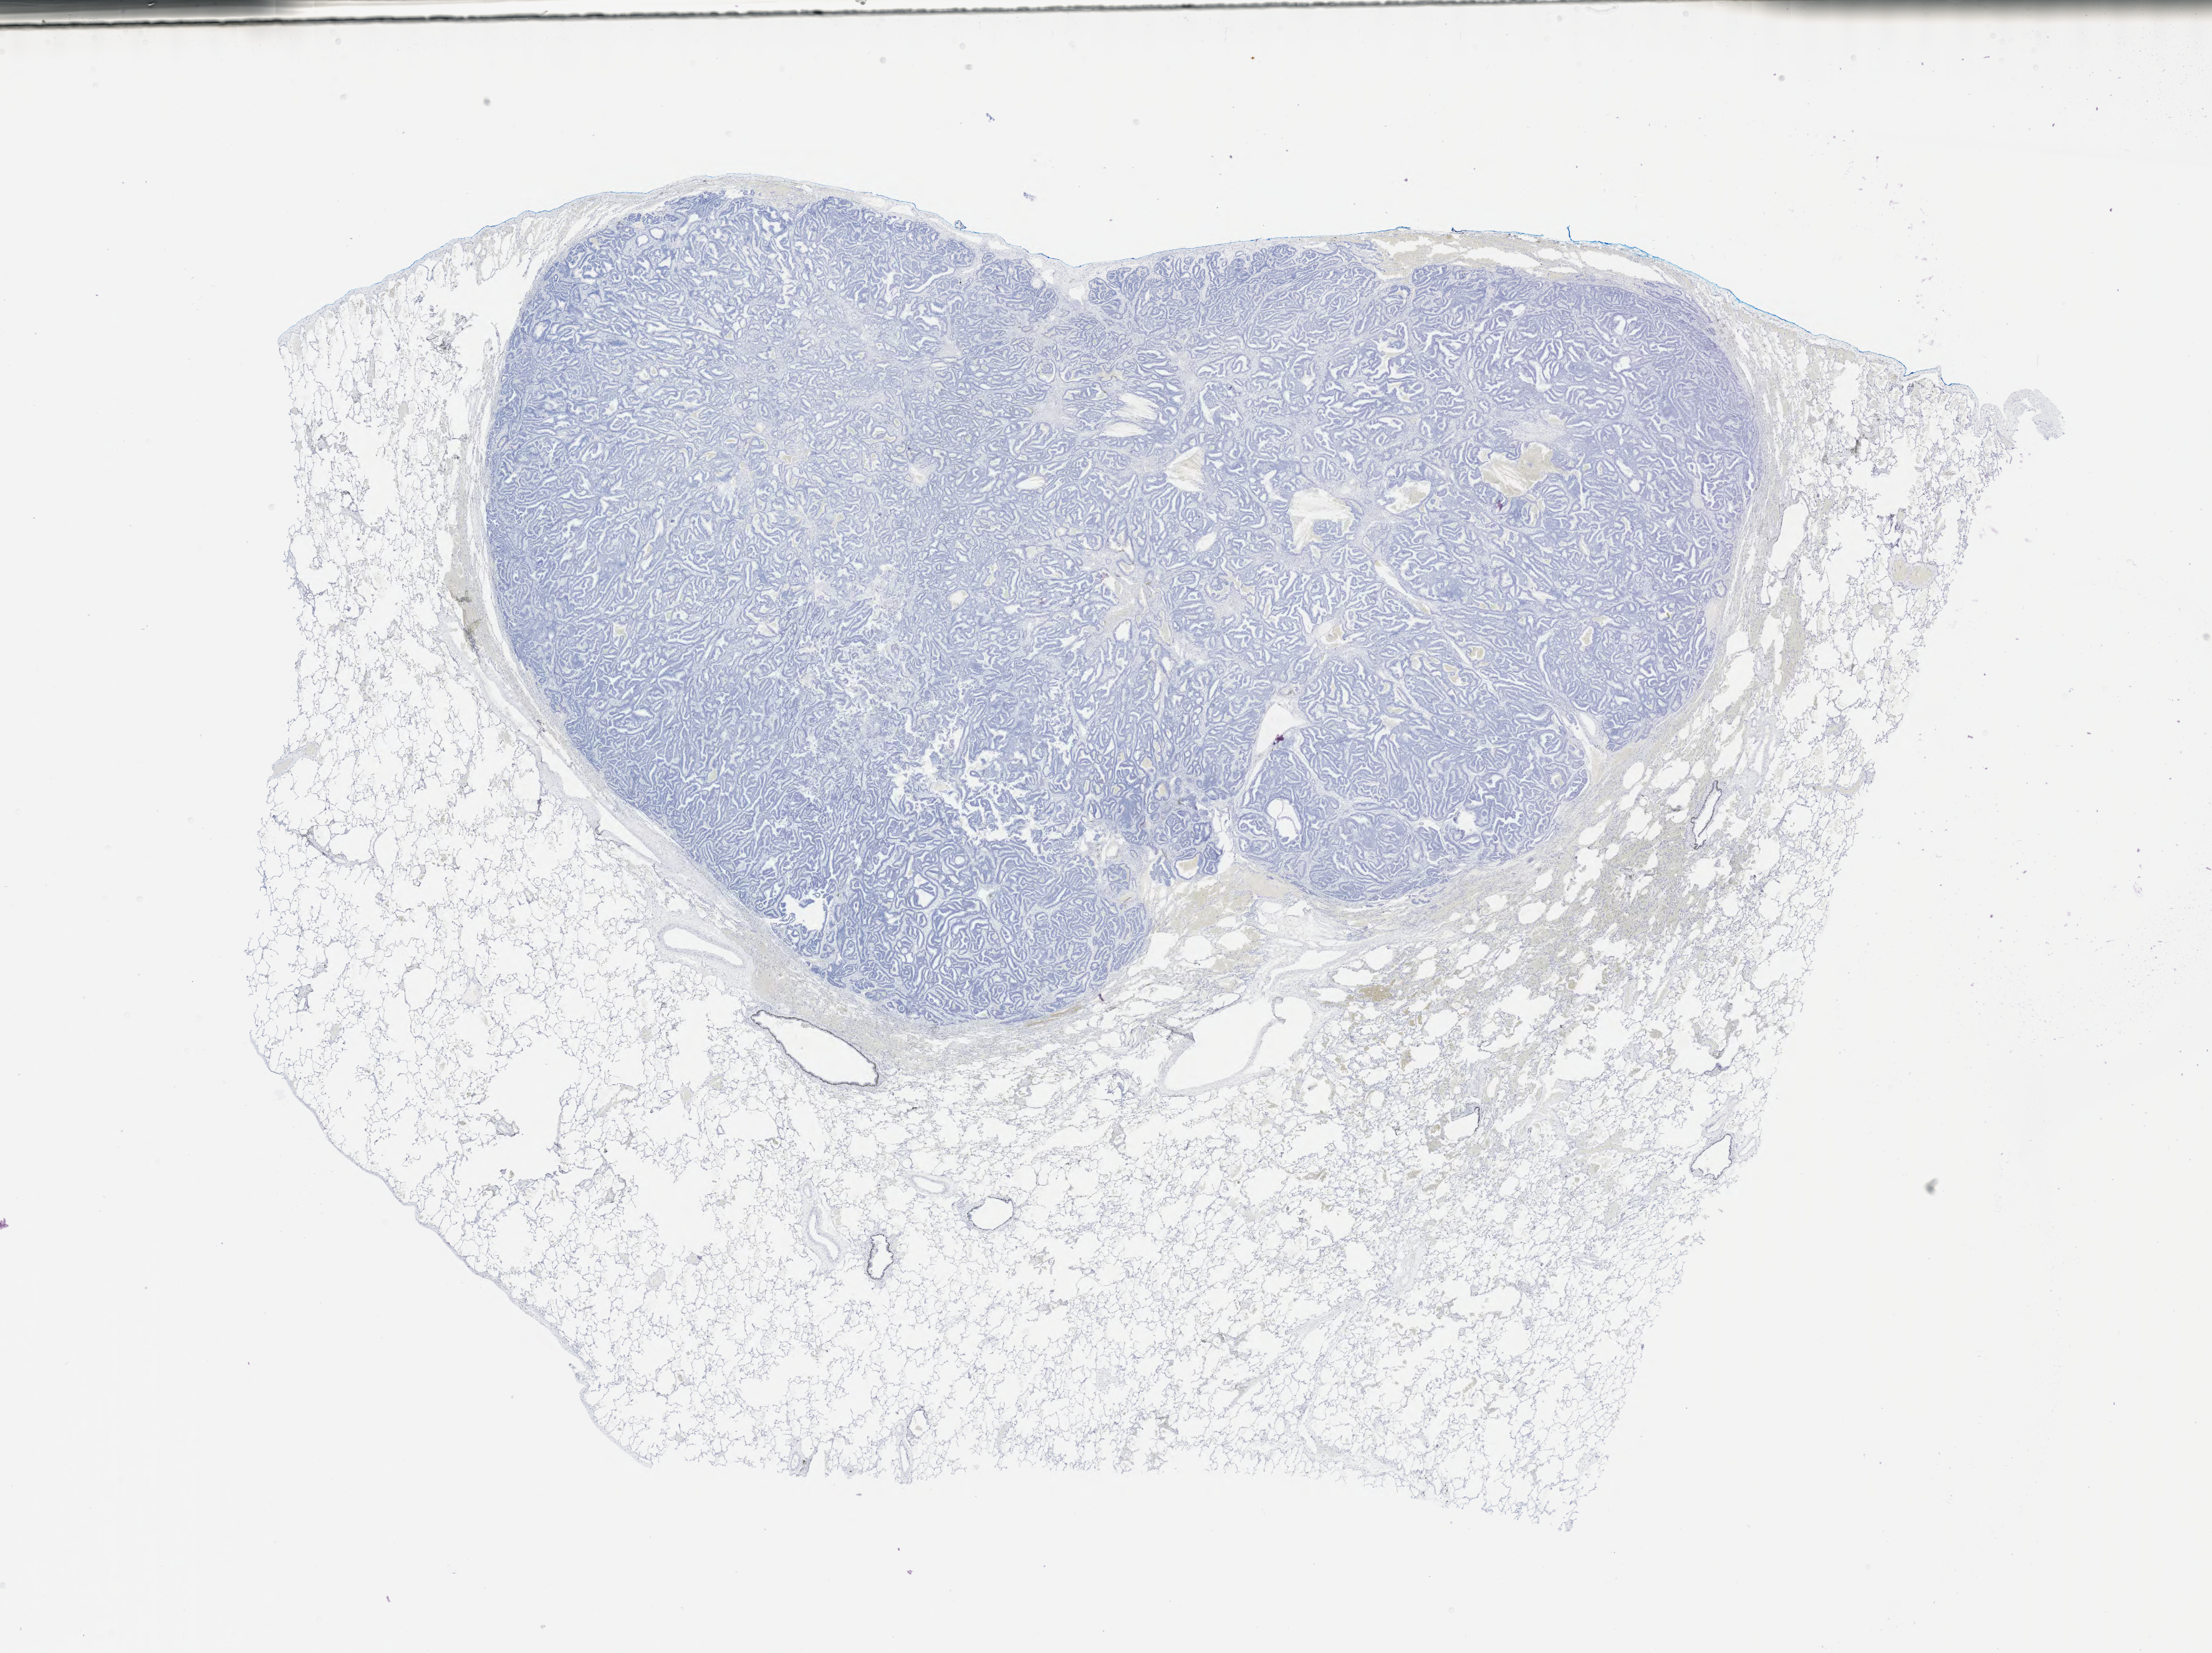
Whole-slide image, immunohistochemical stain for p40, low-resolution overview of the scanned area, about 28.7 x 21.4 mm. Tumor tissue. Anatomic site: lung. Female patient.
Histologic diagnosis: Adenocarcinoma, NOS.